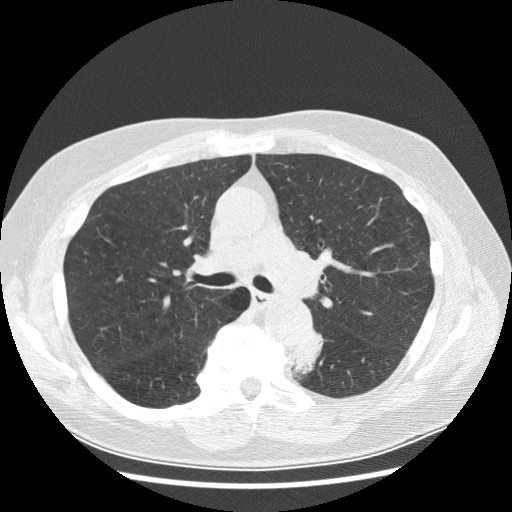
Low-dose screening chest CT, one axial slice; position 181 of 282 along the scan axis; reconstruction kernel STANDARD; 120 kVp; lung window (W 1500 / L -600 HU); 2.5 mm slice thickness; 512 × 512 image matrix, field of view 370 × 370 mm.
Structures marked on this image (expert manual segmentation):
- lesion 1 (tumor, lower lobe of left lung): bounding box [x1, y1, x2, y2] px = [292, 328, 324, 378]